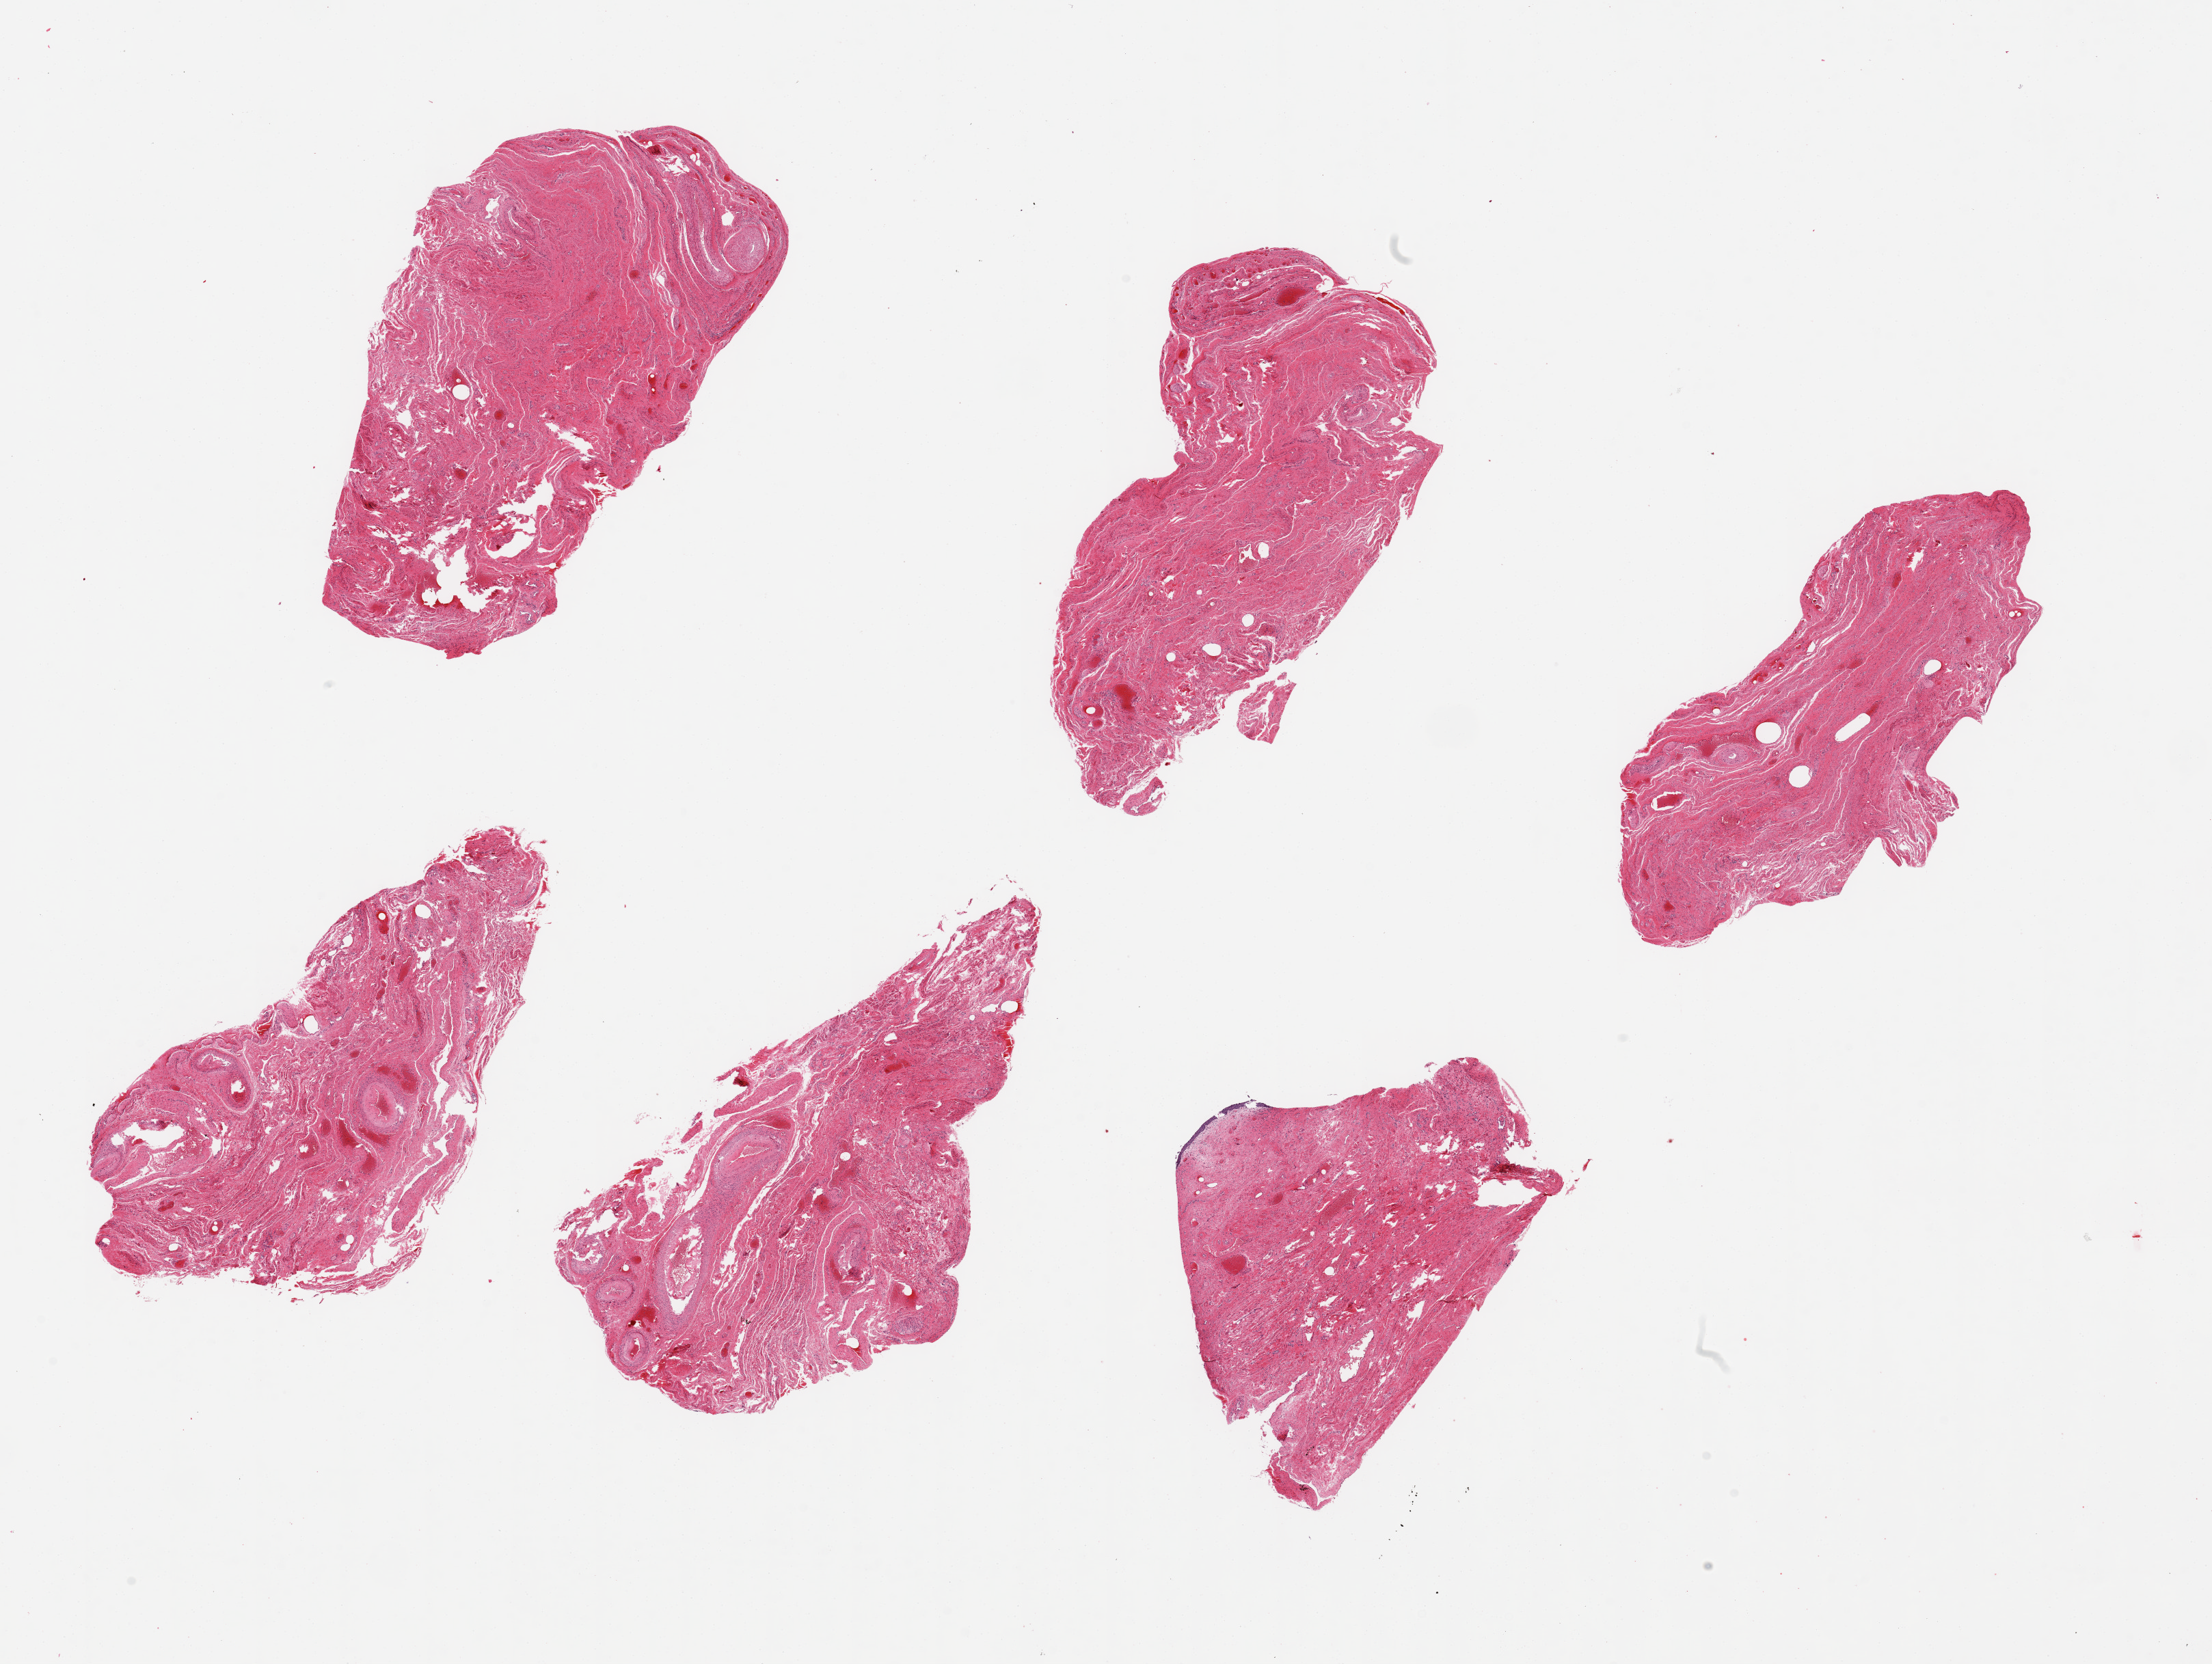
Digitized hematoxylin and eosin (H&E)-stained section — whole scanned area (about 25.6 x 19.3 mm) shown as a low-resolution overview. PAXgene-fixed, paraffin-embedded tissue. Target tissue: vagina. Donor tissue sample. Female donor.
Review note (as recorded): 6 pieces, ~6x2.5mm. One aliquot has trace squamous mucosa, rest completely sloughed.